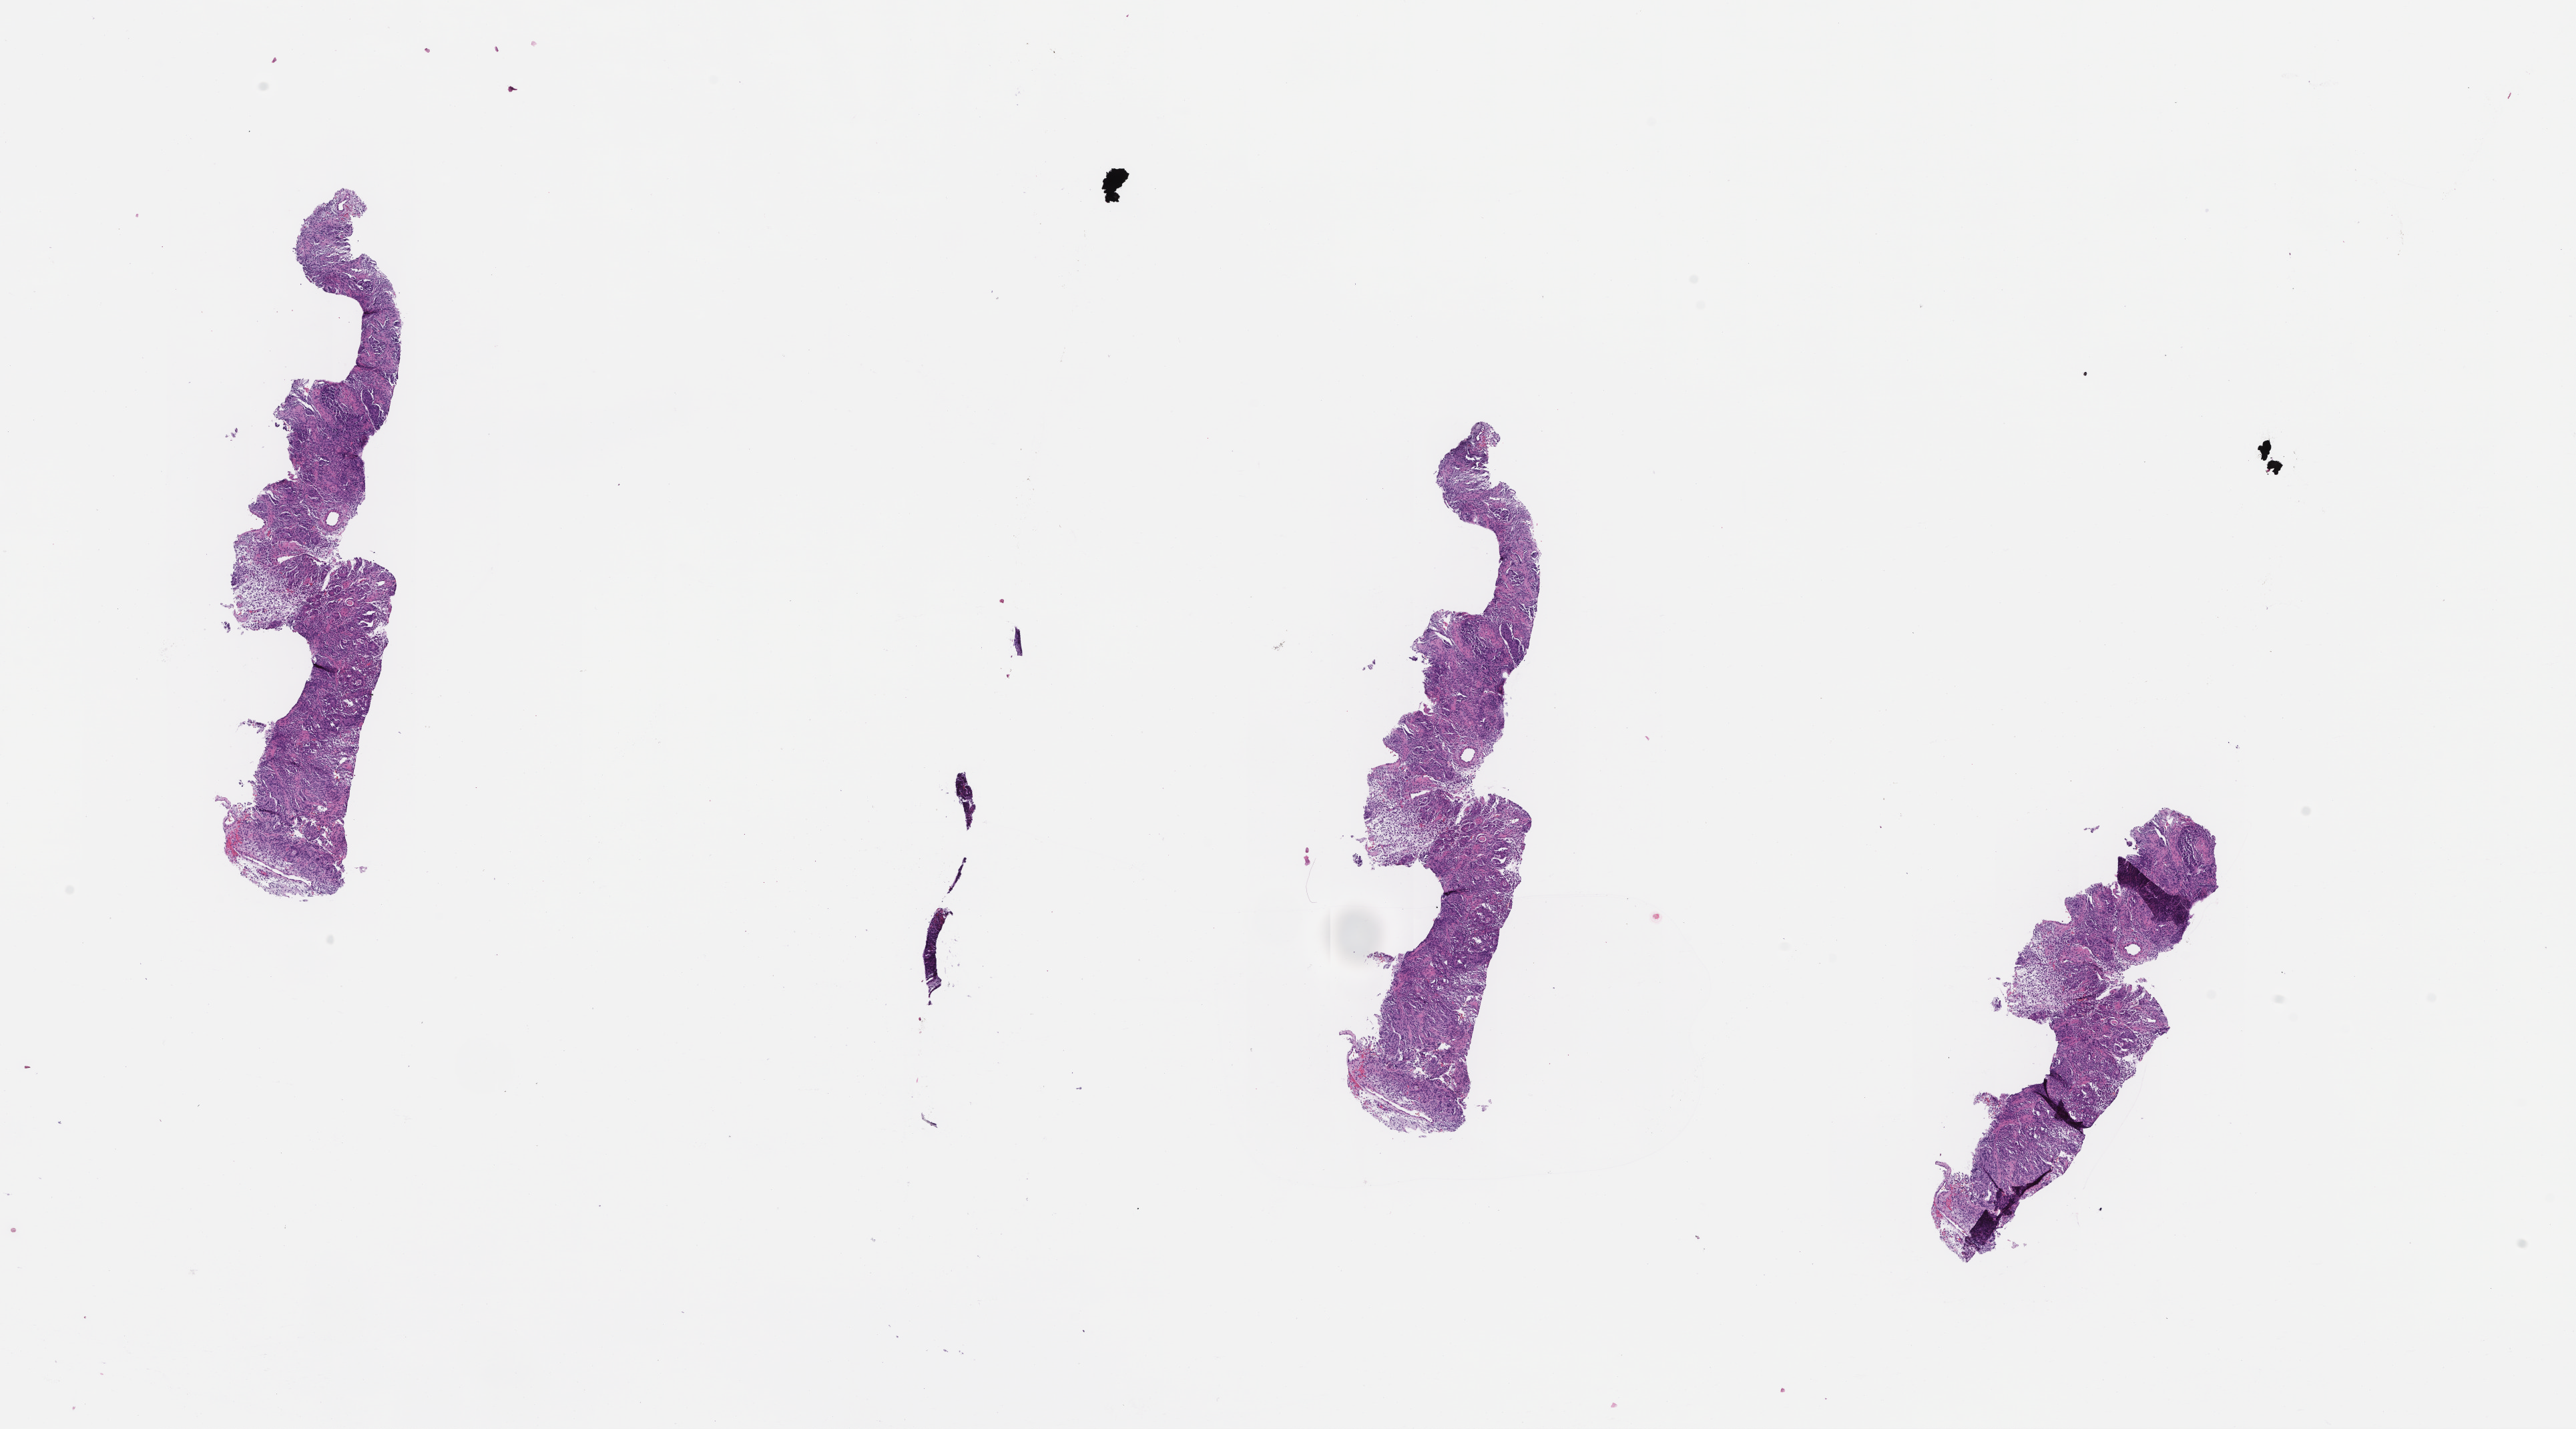
Hematoxylin and eosin (H&E) whole-slide image — shown as a low-resolution overview of the whole scanned area (about 15.6 x 8.6 mm), formalin-fixed, paraffin-embedded (FFPE) tissue, specimen time point: archival tissue. Patient: female.
* this section: metastatic tumor tissue
* patient diagnosis (primary): Colorectal Carcinoma